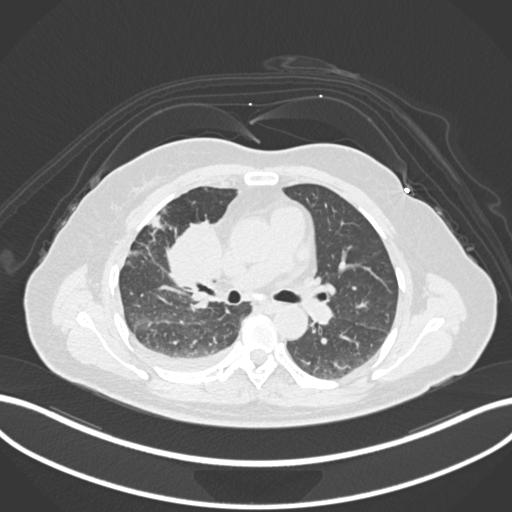
Chest CT, one axial slice; slice 84 of 172 in the series (ordered by position); 120 kVp; lung window (W 1500 / L -600 HU); 512 × 512 image matrix. Patient: female, 52 years. Case-level facts recorded for this patient, not image findings: clinical TNM (as recorded): T3 N1 M1.
Annotated regions visible in this slice (bounding box drawn by a radiologist):
- lung tumour (recorded histology: adenocarcinoma): bounding box (x1, y1, x2, y2) in pixels: (166, 216, 222, 296)